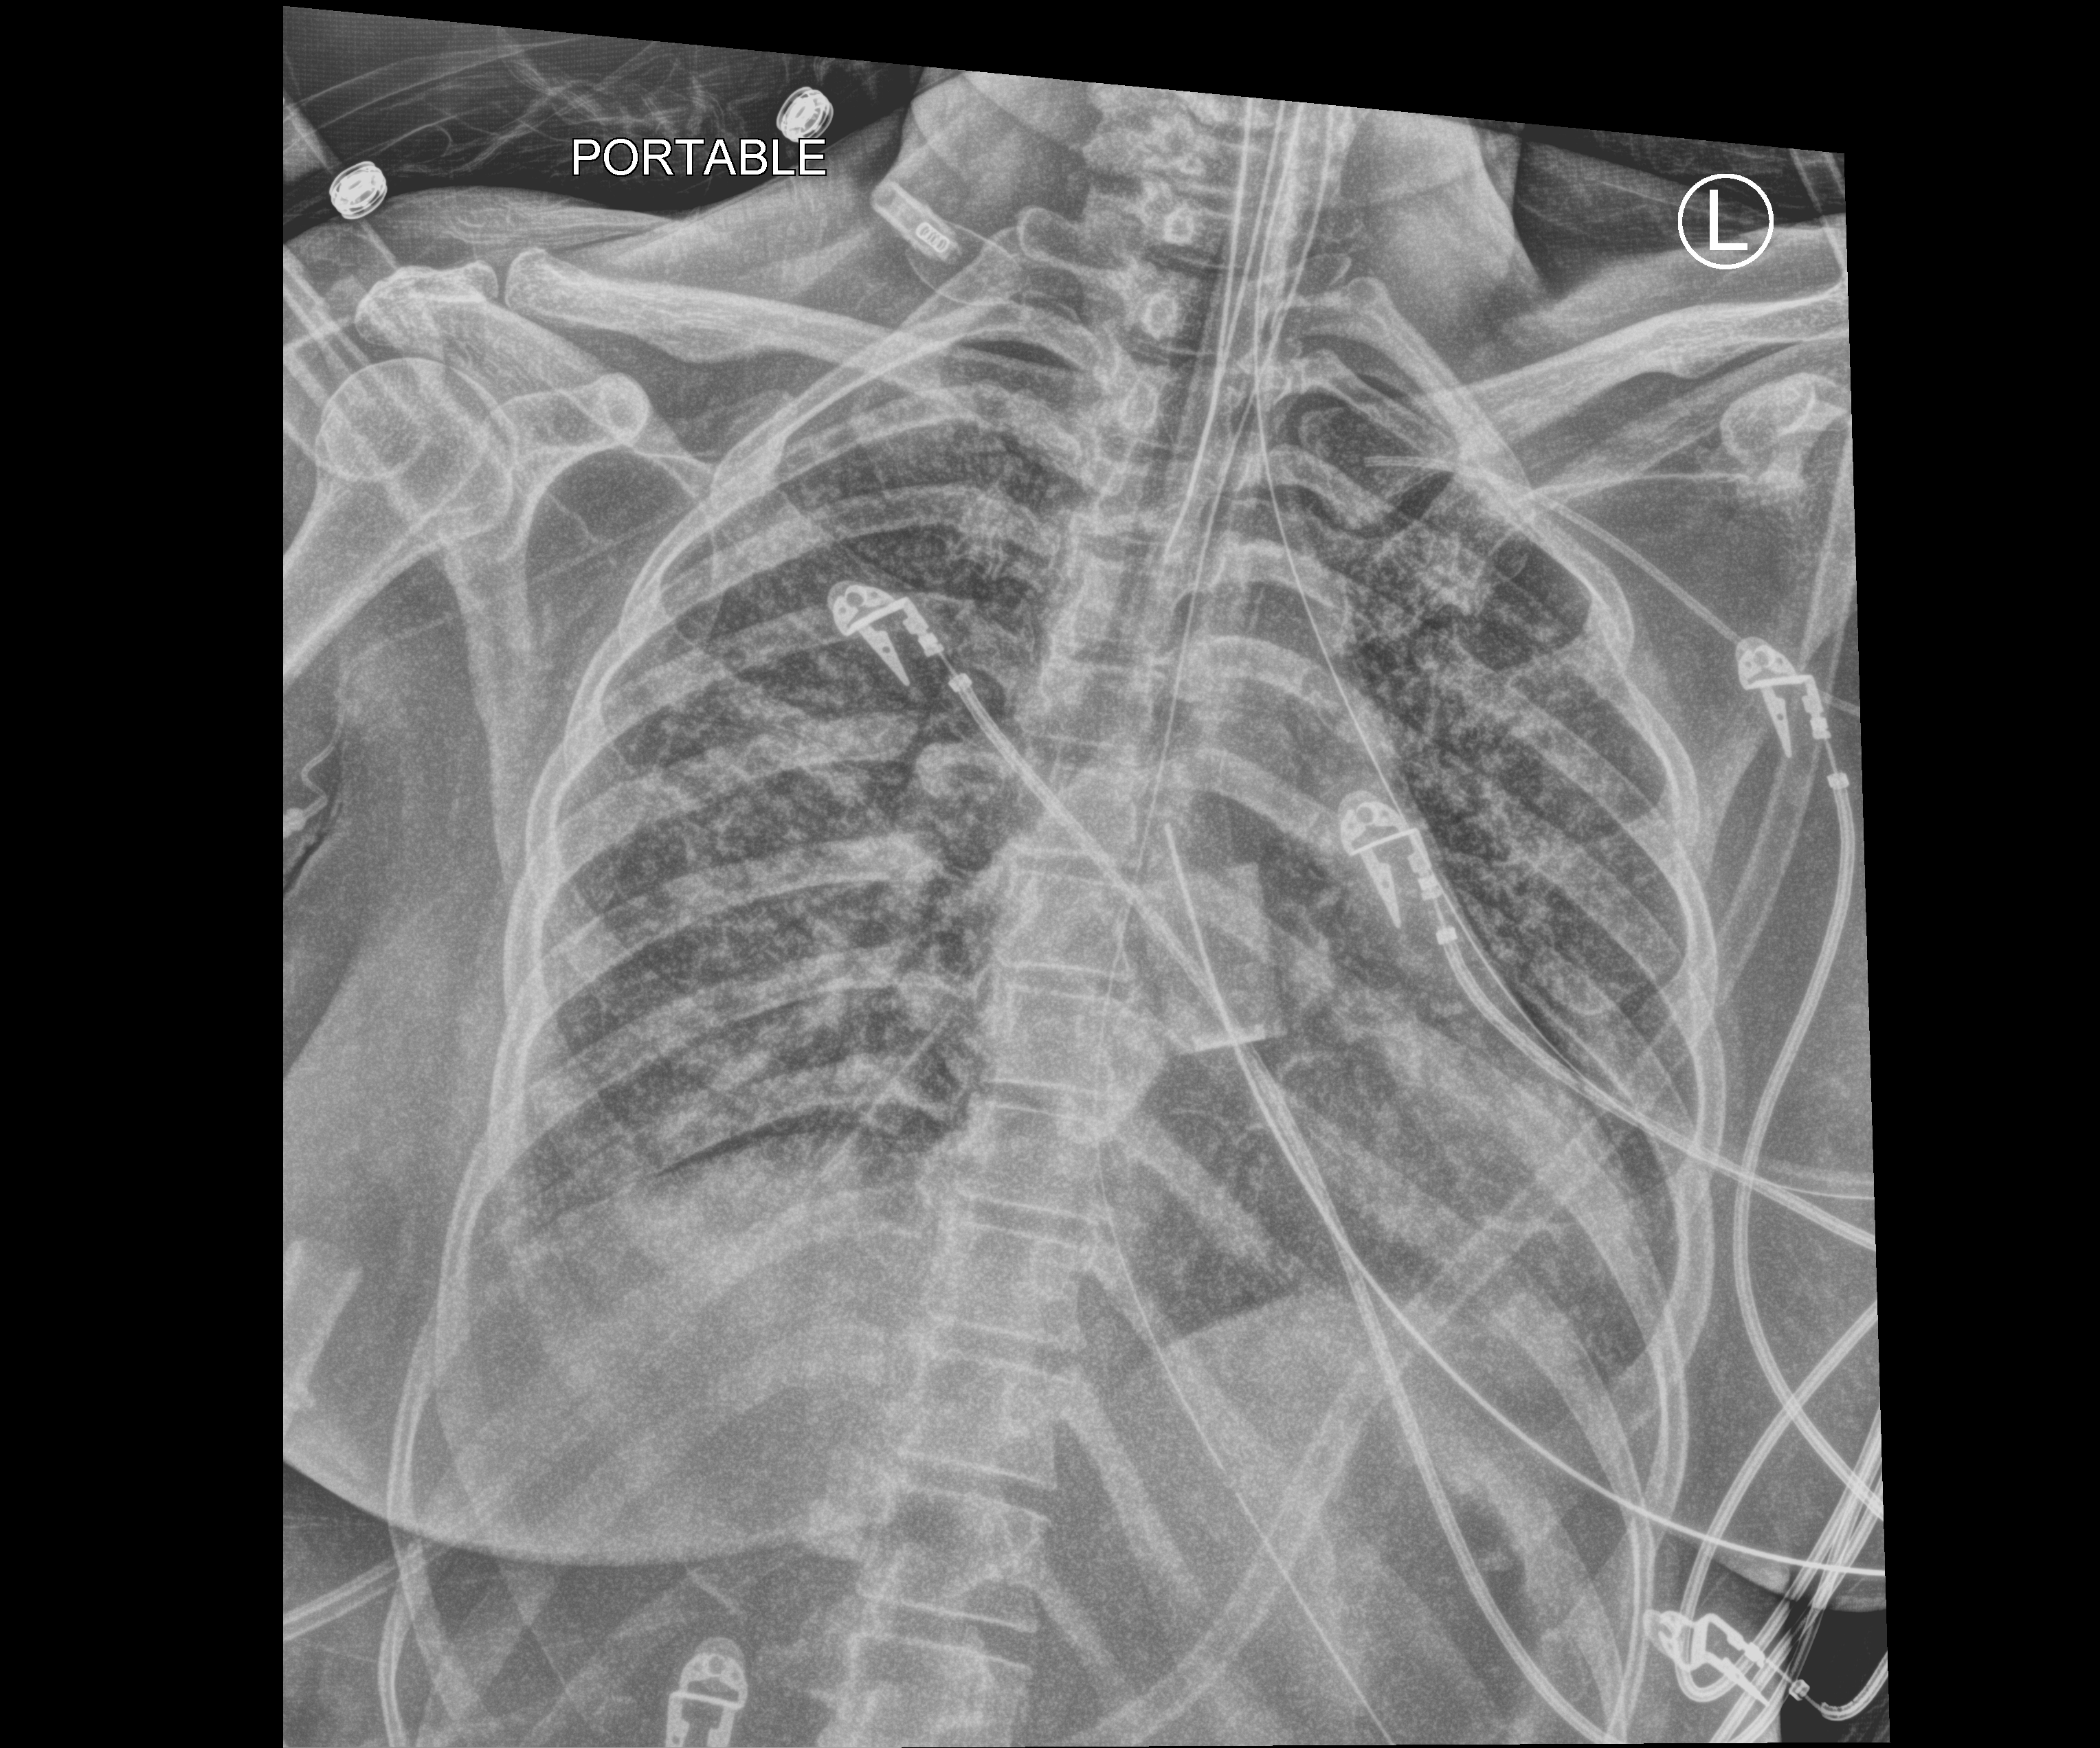
Bedside chest radiograph (computed radiography), anteroposterior (AP) projection. Patient hospitalised with COVID-19; male, aged 18–59 years.
Hospital-stay facts (about this admission, not read from this image; timing relative to this image not recorded): admitted to intensive care during this hospital stay: yes.